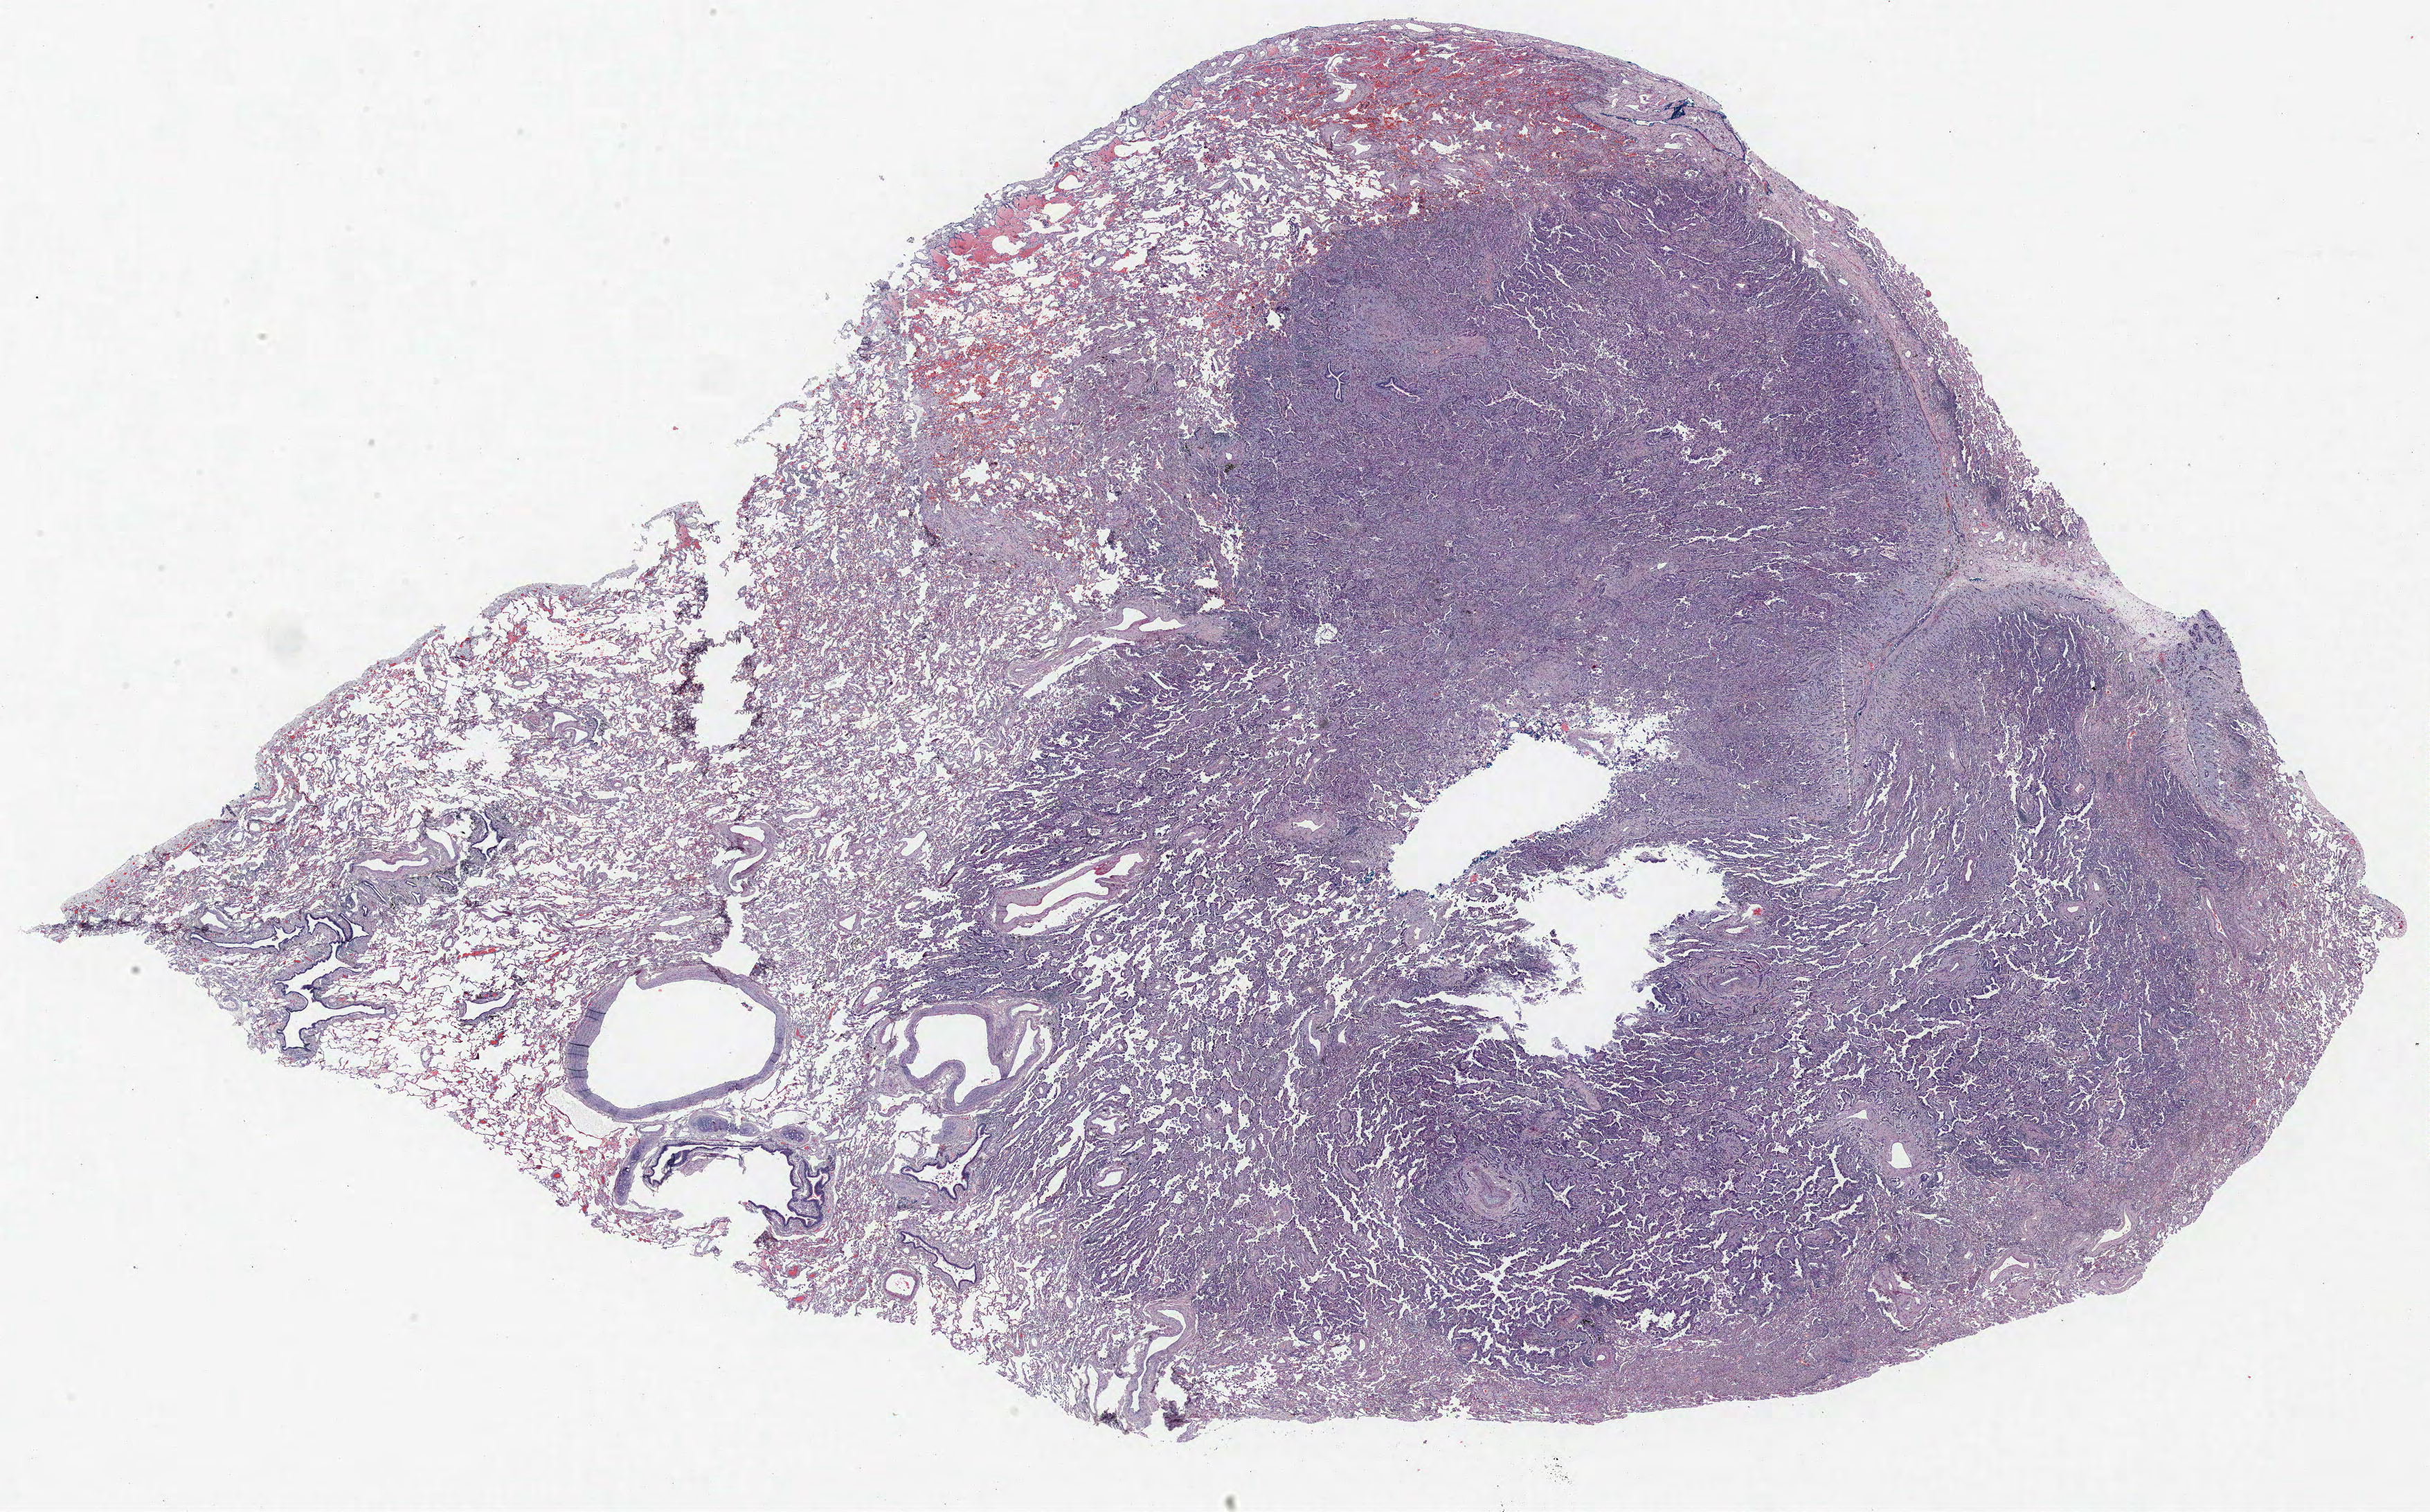
H&E-stained whole-slide image — a low-resolution overview of the entire scanned area, about 28.1 x 17.5 mm; FFPE section; lung. Female patient, aged 56 at enrolment.
Participant's lung-cancer diagnosis: Bronchiolo-alveolar adenocarcinoma, NOS.